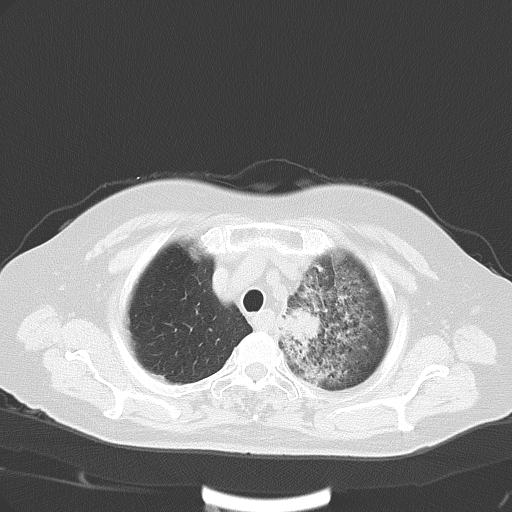
Chest CT, one axial slice; 120 kVp; lung window (W 1500 / L -600 HU); 512 × 512 image matrix, field of view 353 × 353 mm. Patient: female, 65 years. Case-level facts recorded for this patient, not image findings: clinical TNM (as recorded): T2b N1 M0.
Outlined on this slice (bounding box drawn by a radiologist):
- lung tumour (recorded histology: adenocarcinoma): bounding box (x1, y1, x2, y2) in pixels: (282, 306, 324, 343)